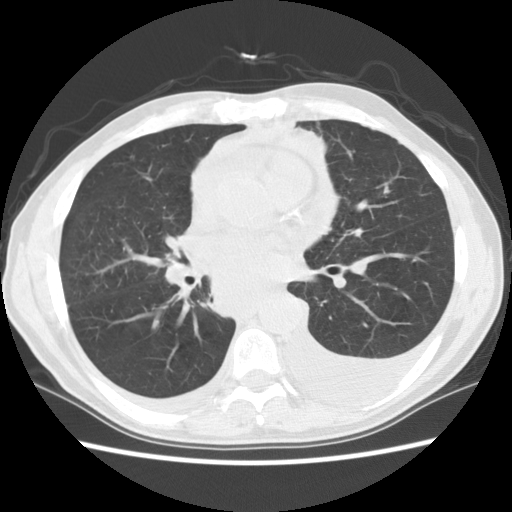
Low-dose screening chest CT, axial slice; baseline screening round; lung window (W 1500 / L -600 HU); 2.5 mm slice thickness; slice 60 of 135 in the series; 512 × 512 image matrix, field of view 346 × 346 mm. Male participant, aged 60 years at enrolment.
Expert reader's lesion annotation, bounding box (x1, y1, x2, y2) in pixels: (174, 241, 305, 333). No non-calcified nodule or mass ≥4 mm was recorded by the screening reader at this exam. Later outcome: lung cancer diagnosed 12 days after this screen — squamous cell carcinoma, NOS, carina, poorly differentiated (G3), stage IV (AJCC 6th edition).